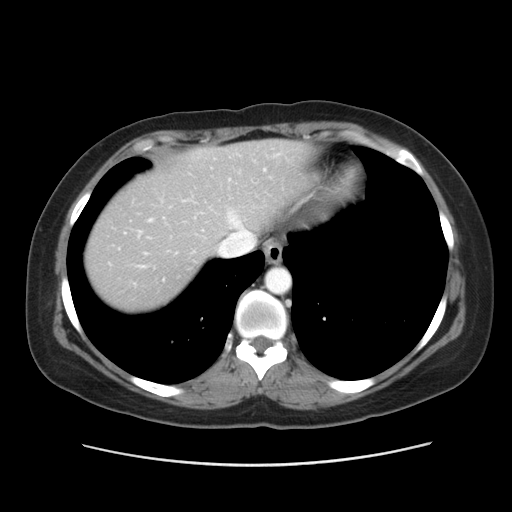
Contrast-enhanced abdominal CT, one axial slice. Slice 44 of 52 in the series (ordered by position). 120 kVp. Intravenous contrast given. Soft-tissue window (W 400 / L 40 HU). 5 mm slice thickness. 512 × 512 image matrix, field of view 362 × 362 mm. Female patient, age 48 years. Case-level facts recorded for this patient, not image findings: diagnosis: colorectal cancer liver metastases, imaged before liver resection; multiple liver metastases: yes; largest metastasis: 4.5 cm; disease in both lobes: yes.
Annotated regions visible in this slice (expert manual segmentation):
- hepatic veins: bounding box (x1, y1, x2, y2) in pixels: (138, 169, 265, 282)
- liver: (86, 140, 307, 309)
- planned liver remnant (the part of the liver to remain after resection): (163, 140, 308, 233)